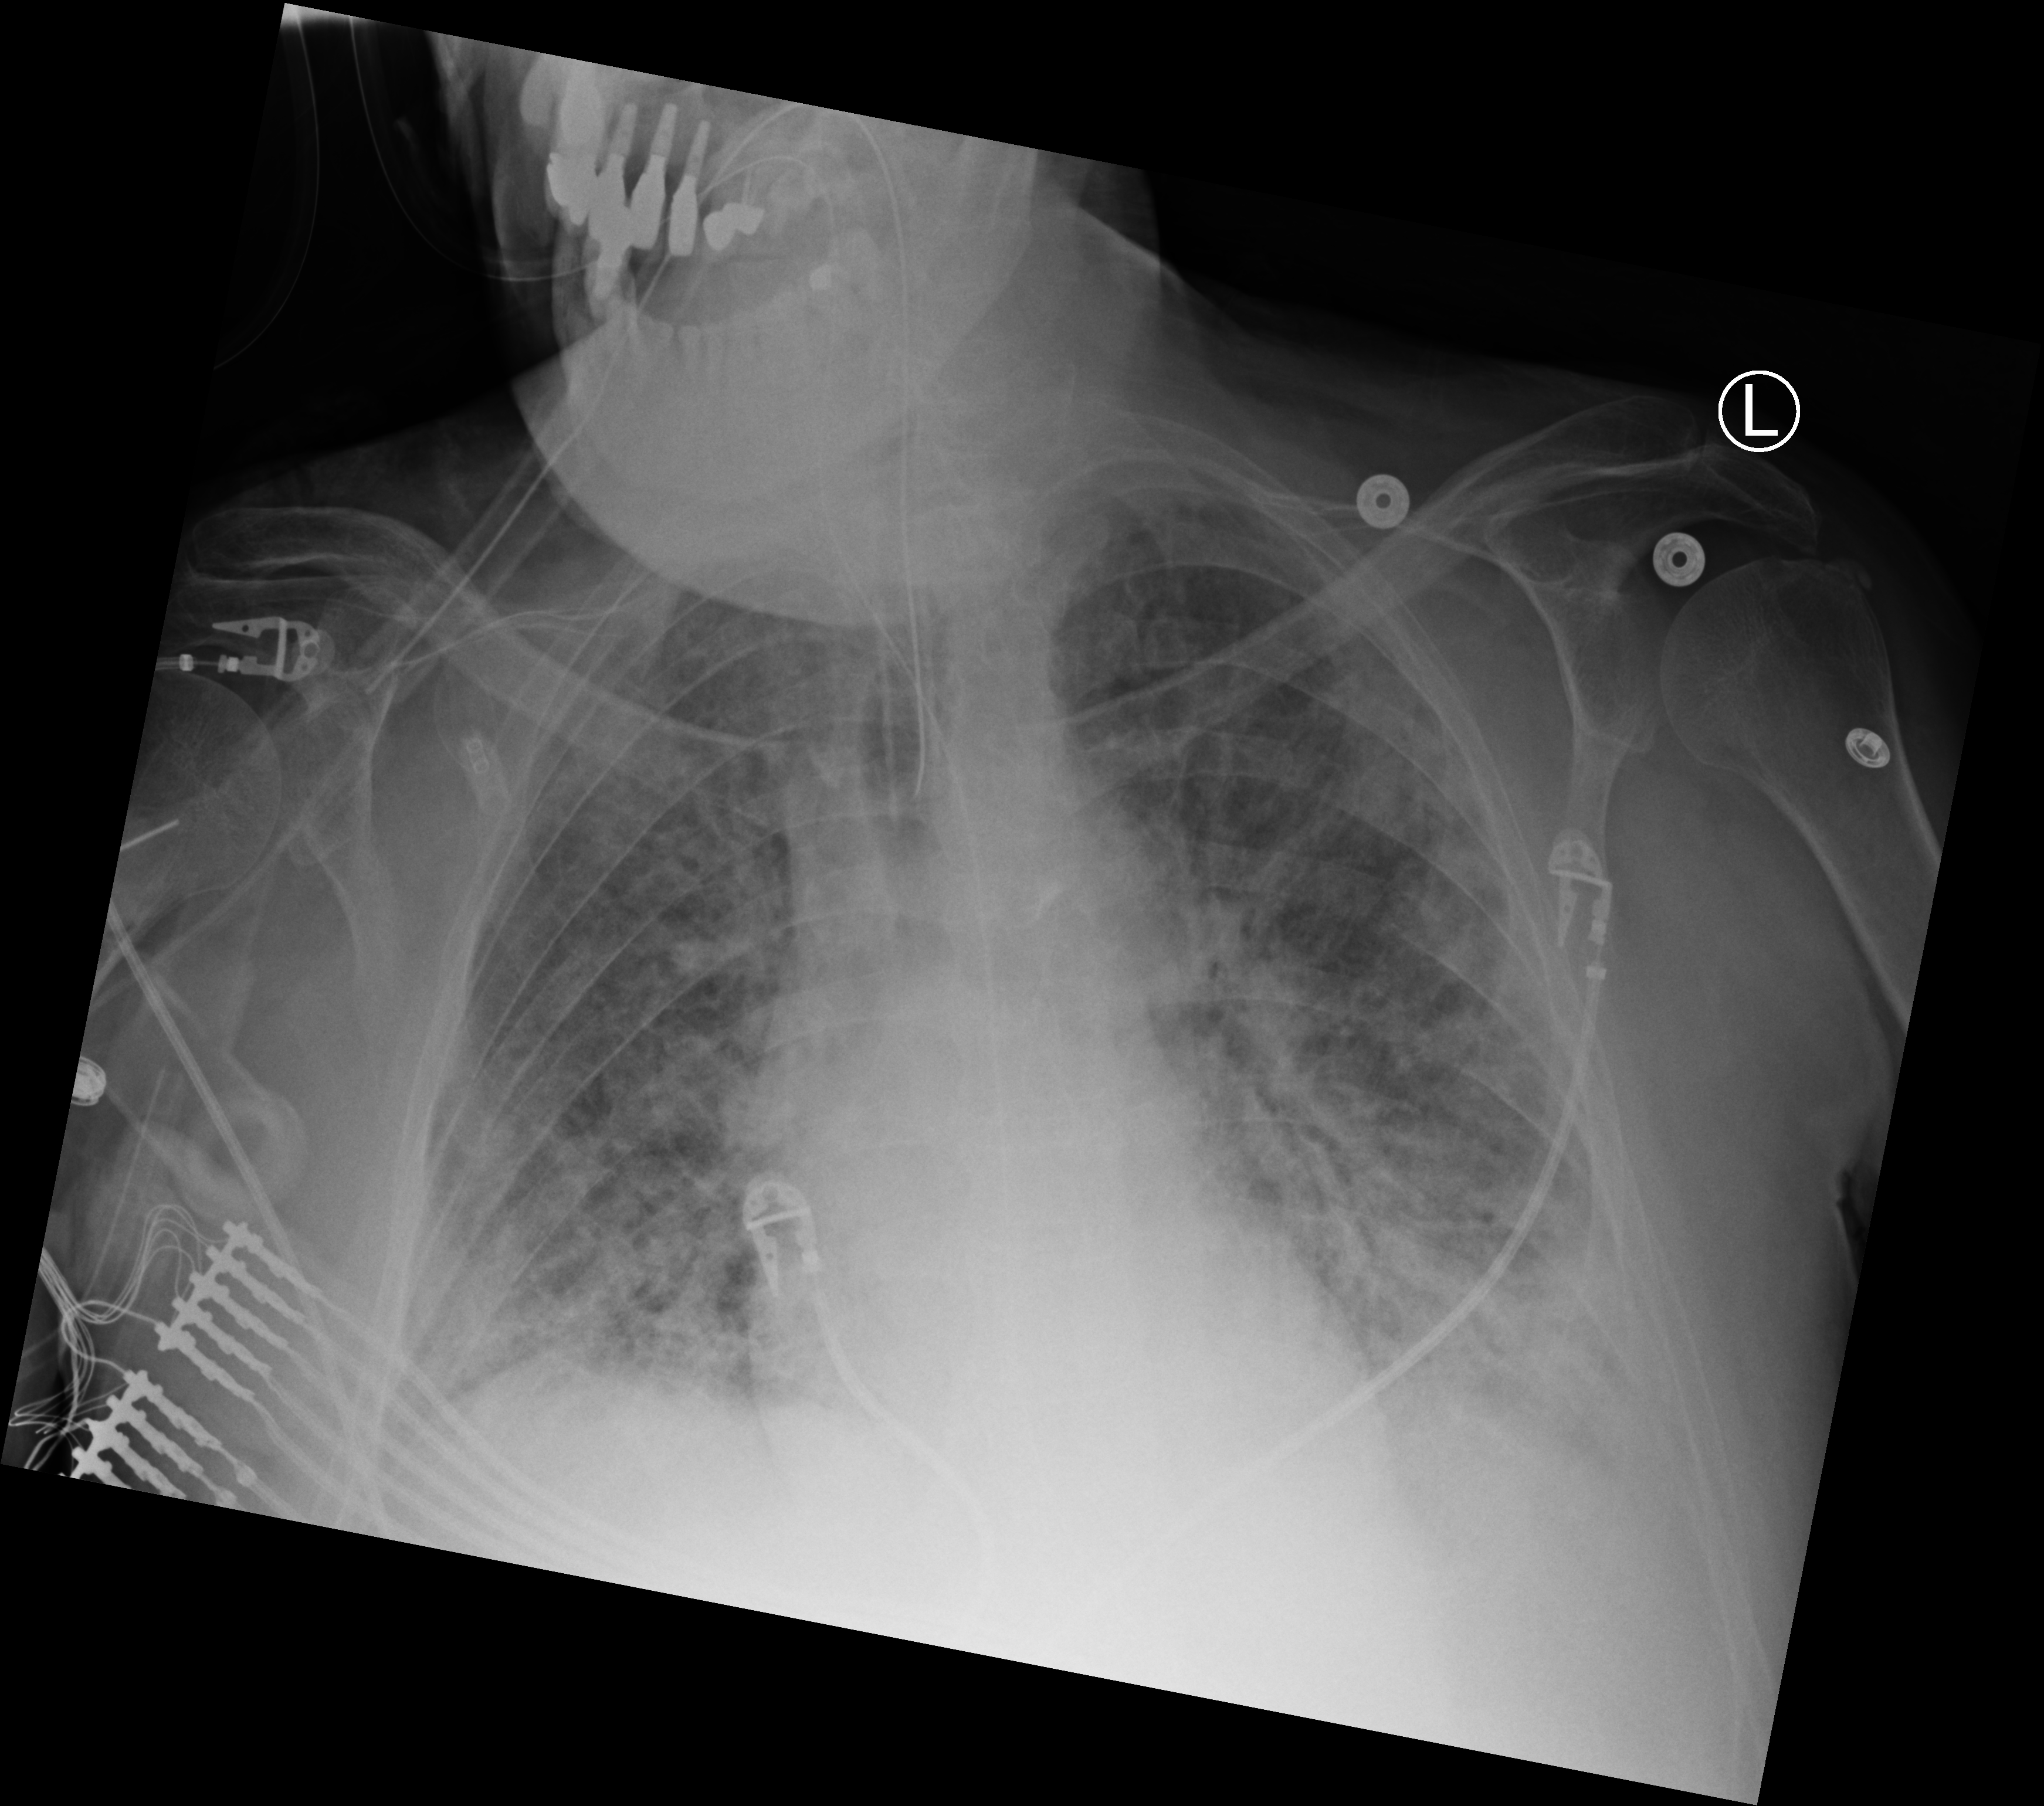
Chest X-ray (portable), anteroposterior (AP) projection. Male patient hospitalised with COVID-19, age 60–74 years.
From the hospital-stay record, not from the radiograph (when in the stay this image was taken is not recorded): admitted to intensive care during this hospital stay: yes.